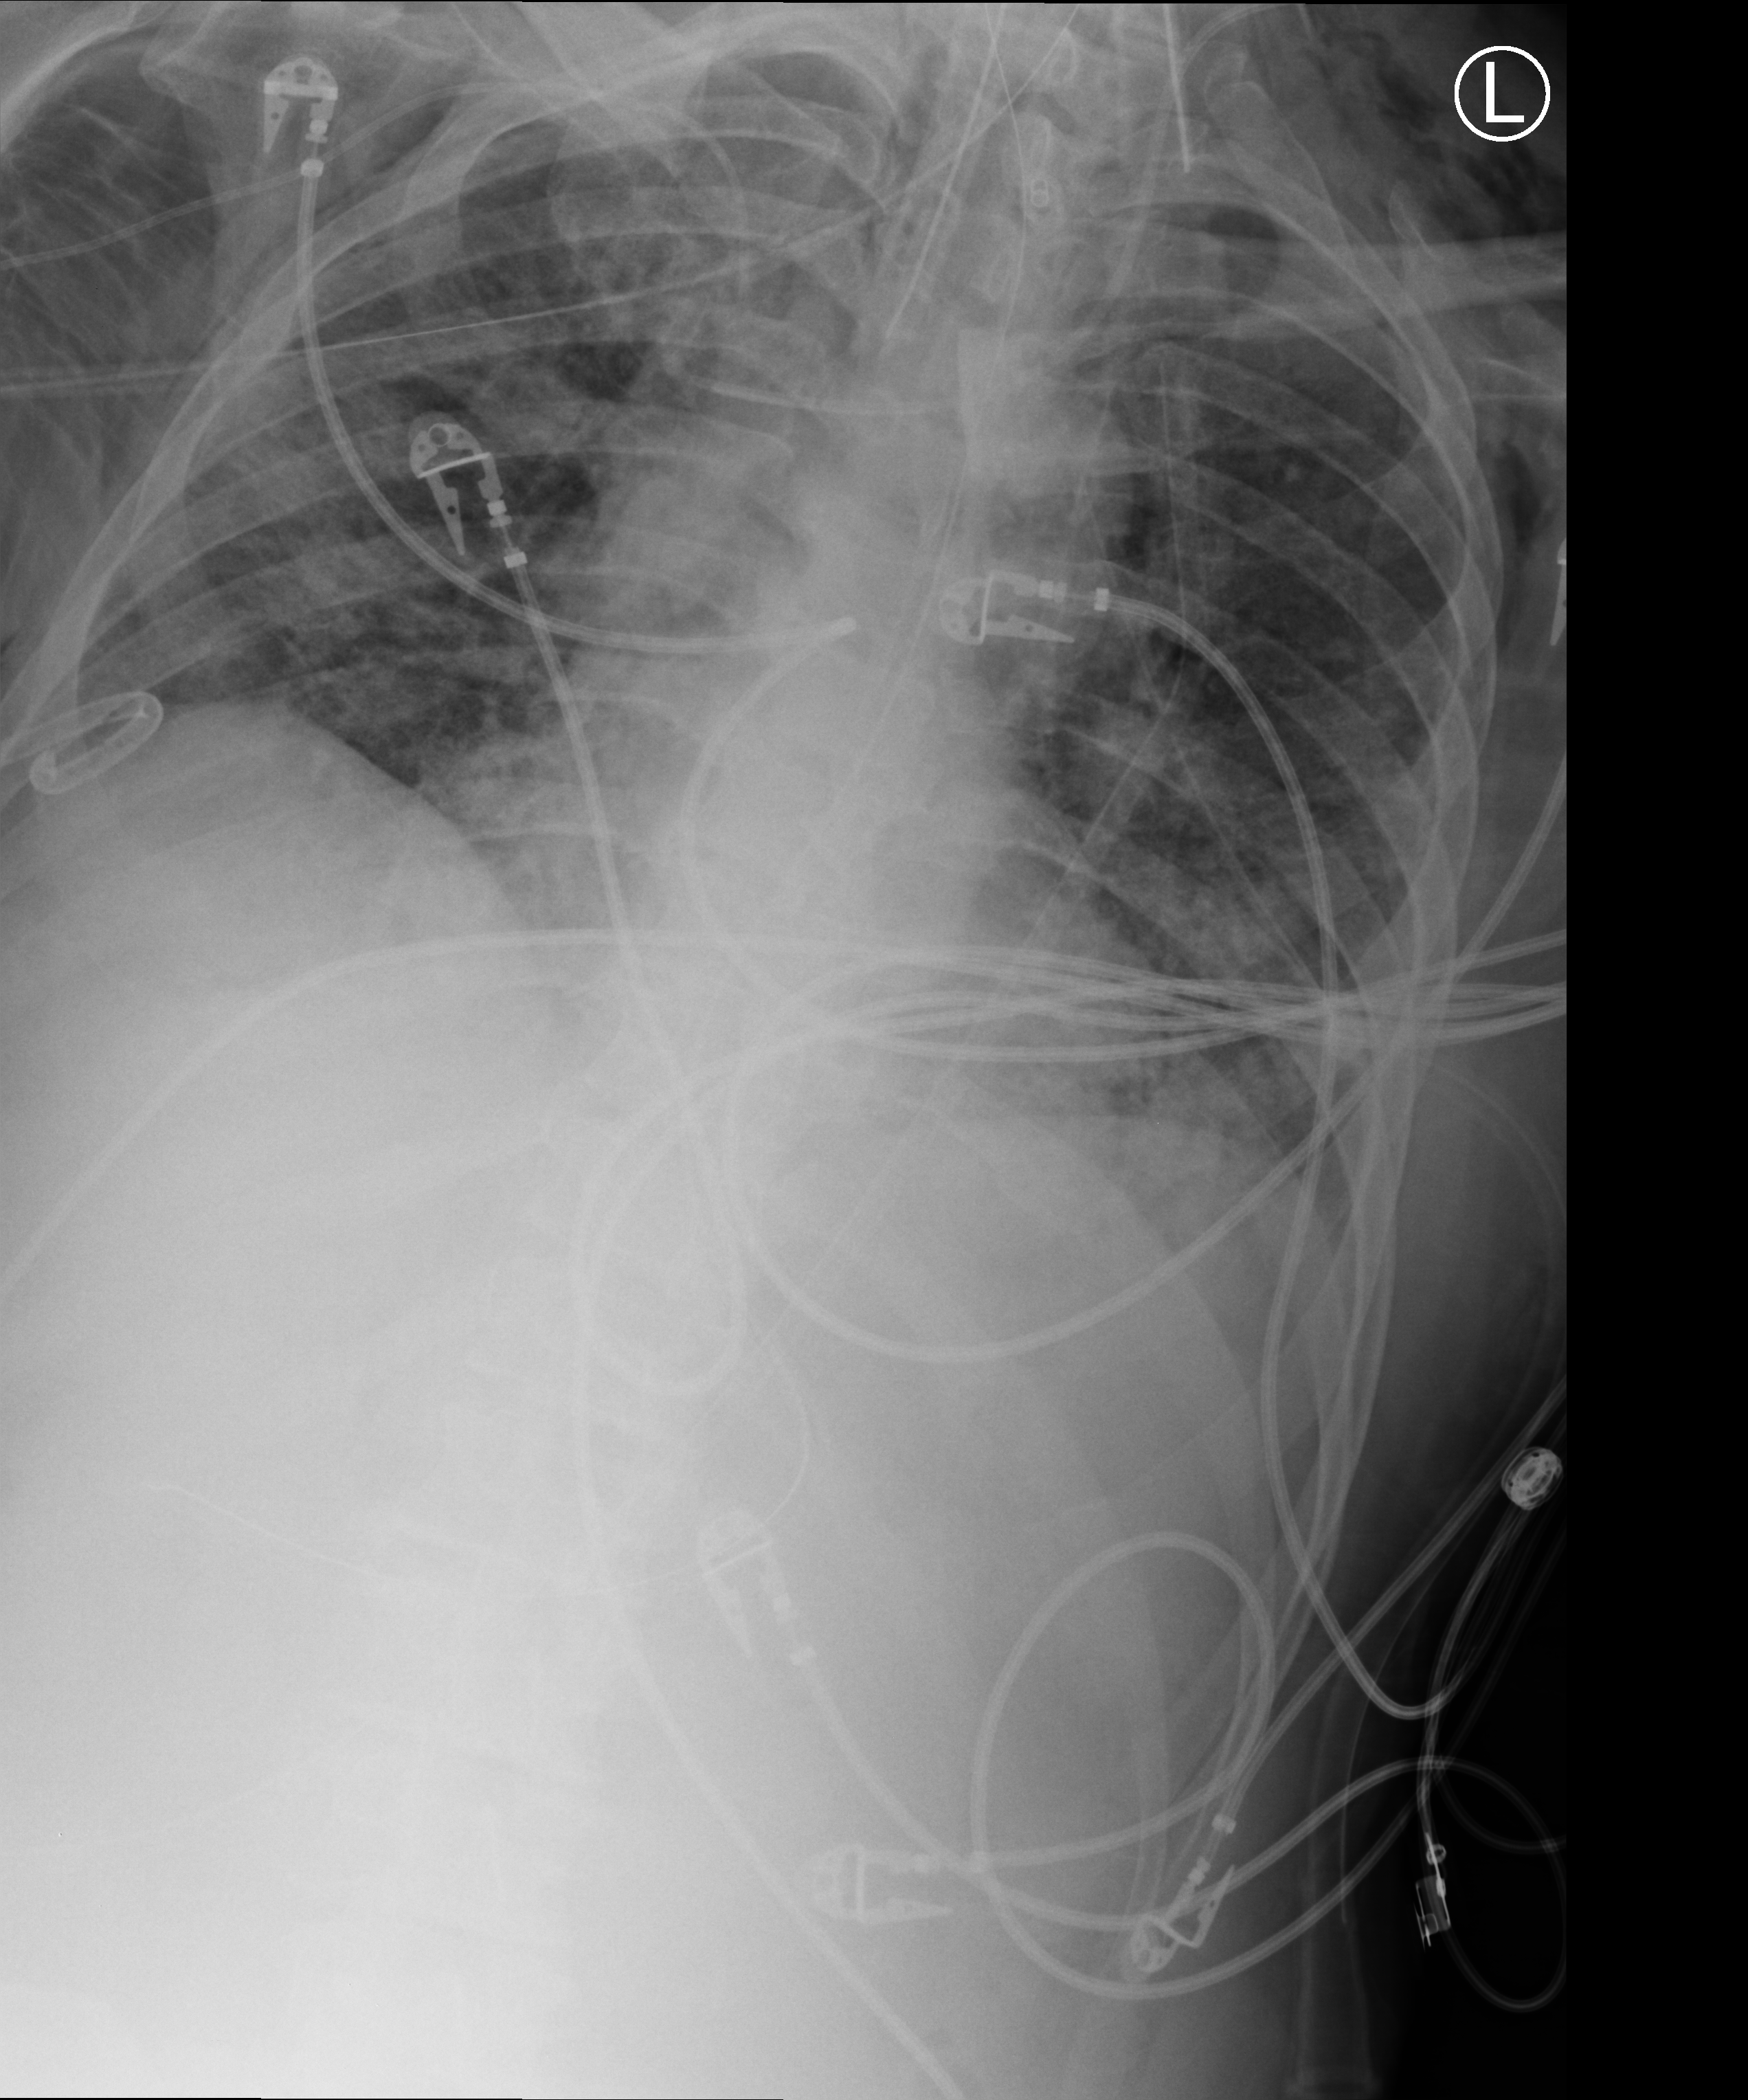
Portable chest radiograph, anteroposterior (AP) projection. Male patient hospitalised with COVID-19, age 18–59 years.
From the hospital-stay record, not from the radiograph (when in the stay this image was taken is not recorded): admitted to intensive care during this hospital stay: yes; mechanically ventilated during this hospital stay: yes.